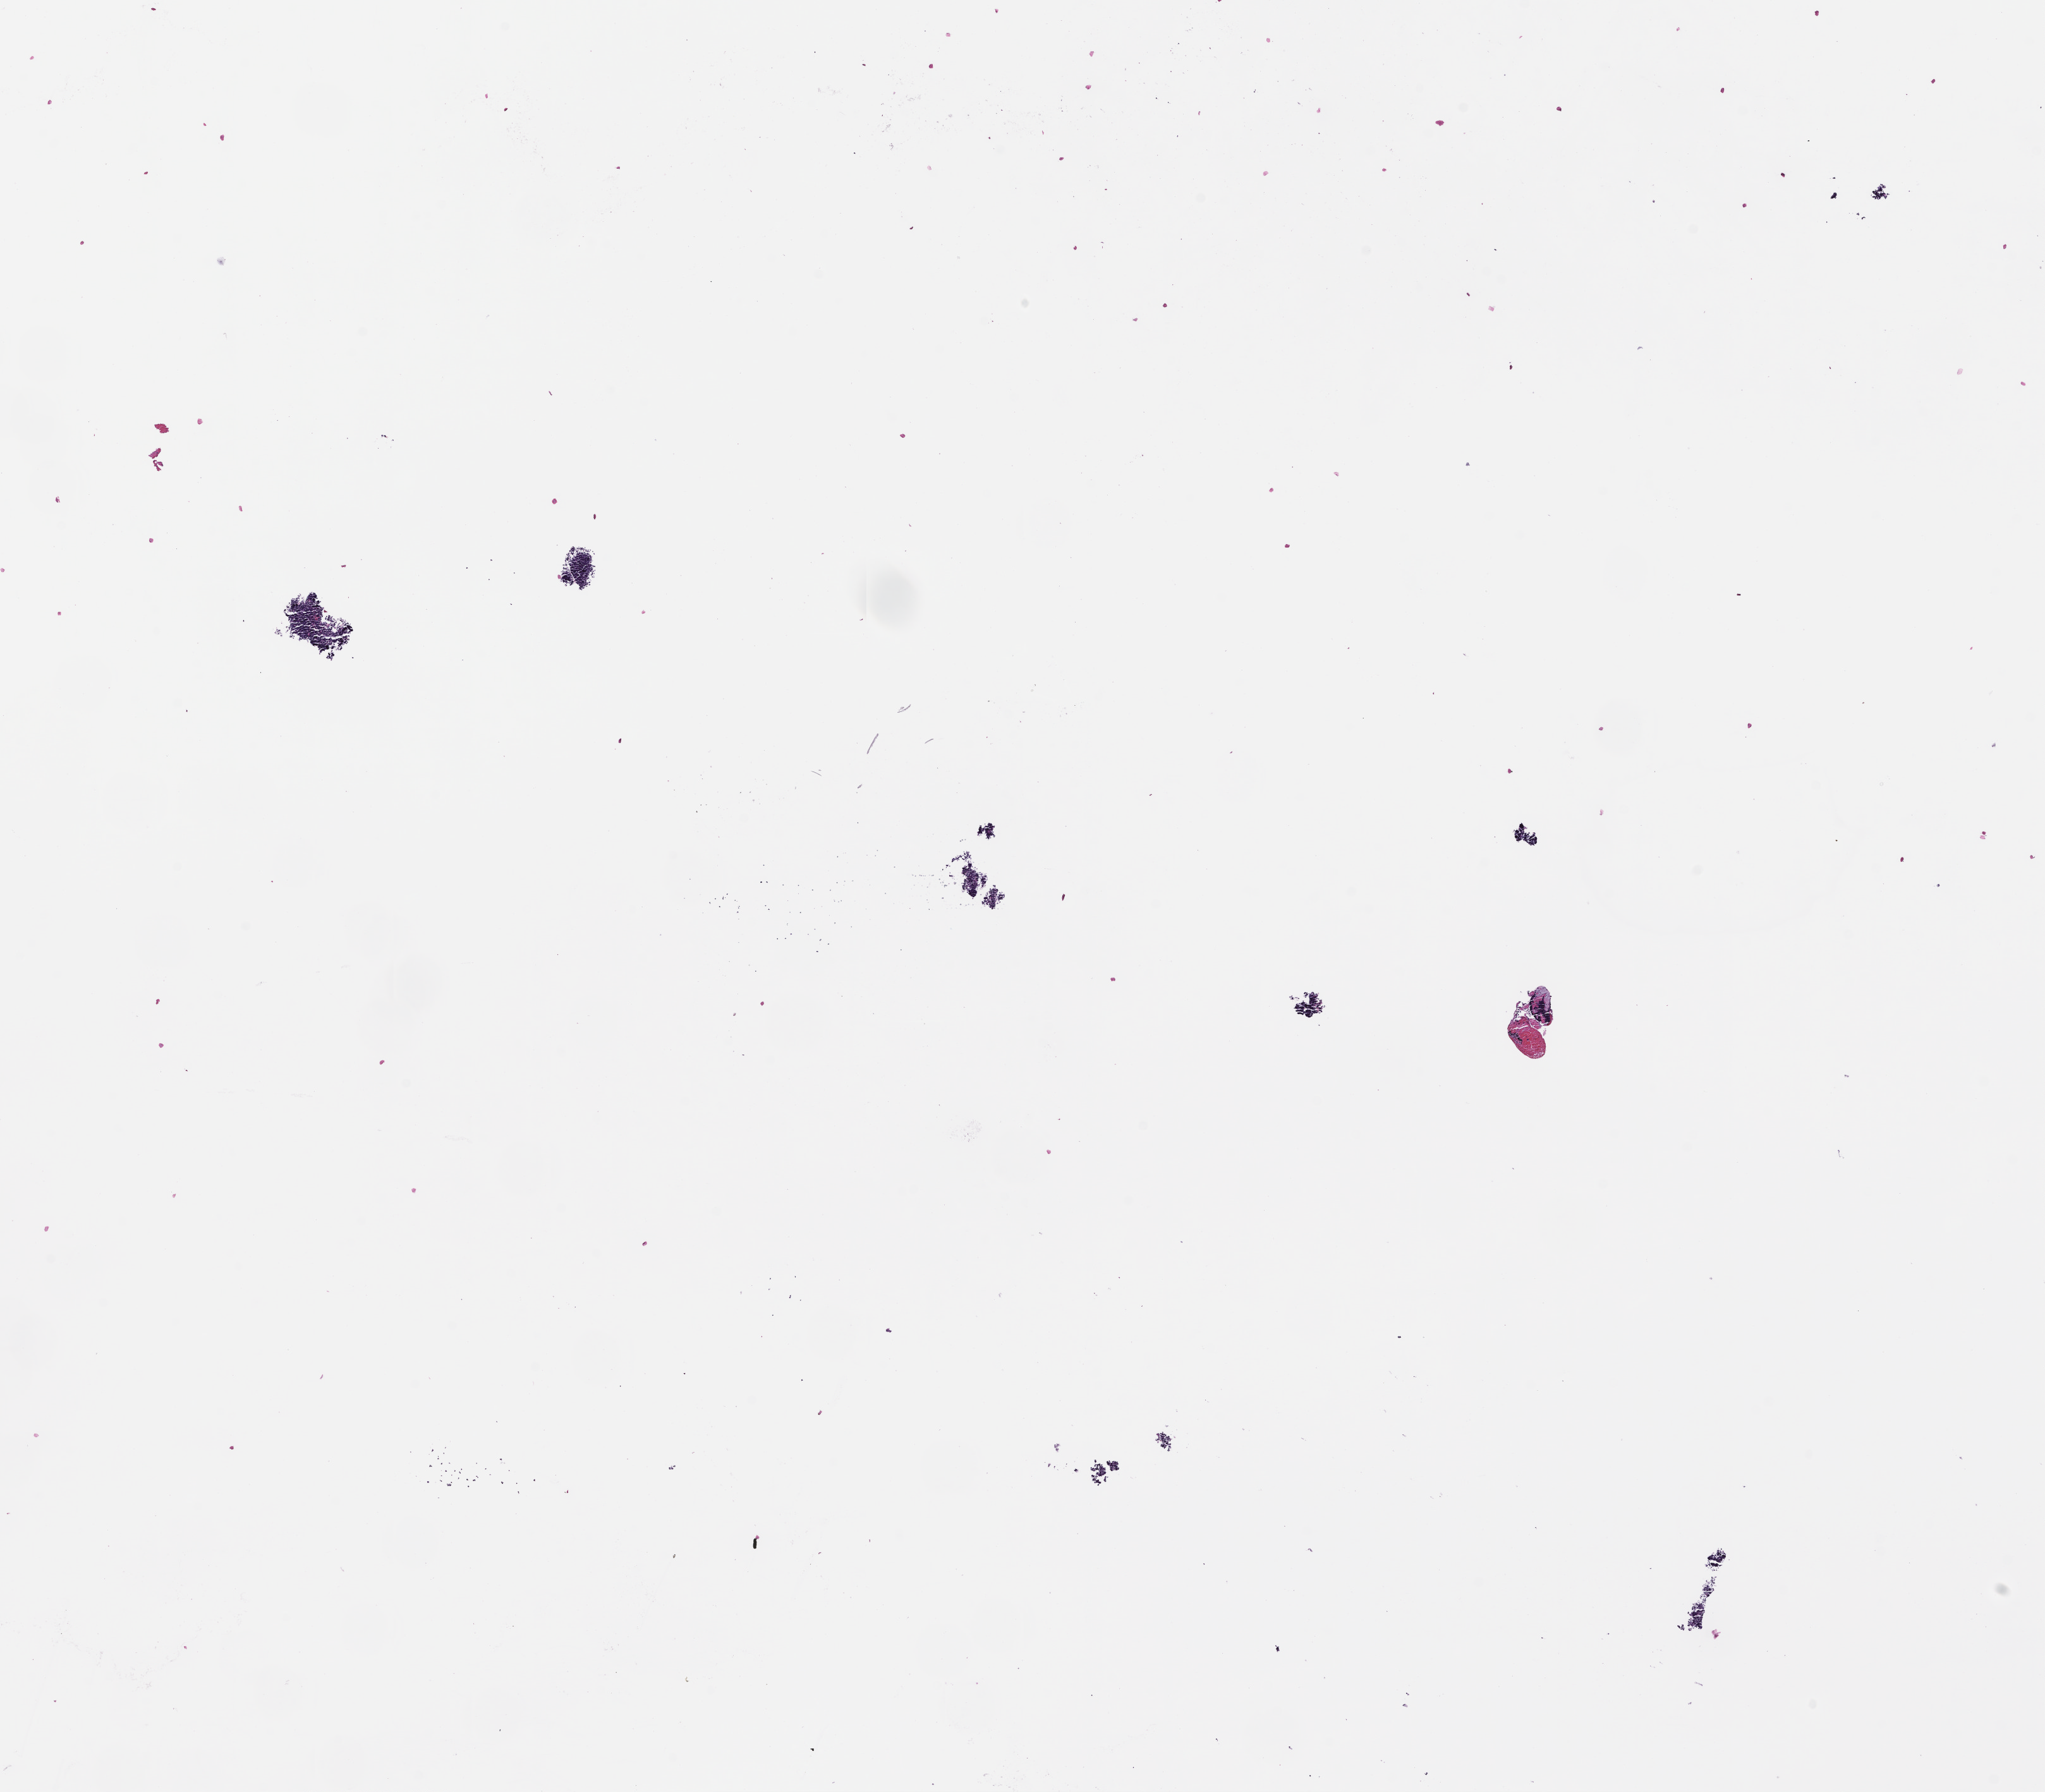
Digitized hematoxylin and eosin (H&E)-stained section — whole scanned area (about 13.1 x 11.5 mm) shown as a low-resolution overview, FFPE section, specimen time point: collected at baseline (before treatment). Patient: female.
This section: metastasis (sampled organ not recorded). Primary diagnosis of the patient: Small Cell Lung Carcinoma.